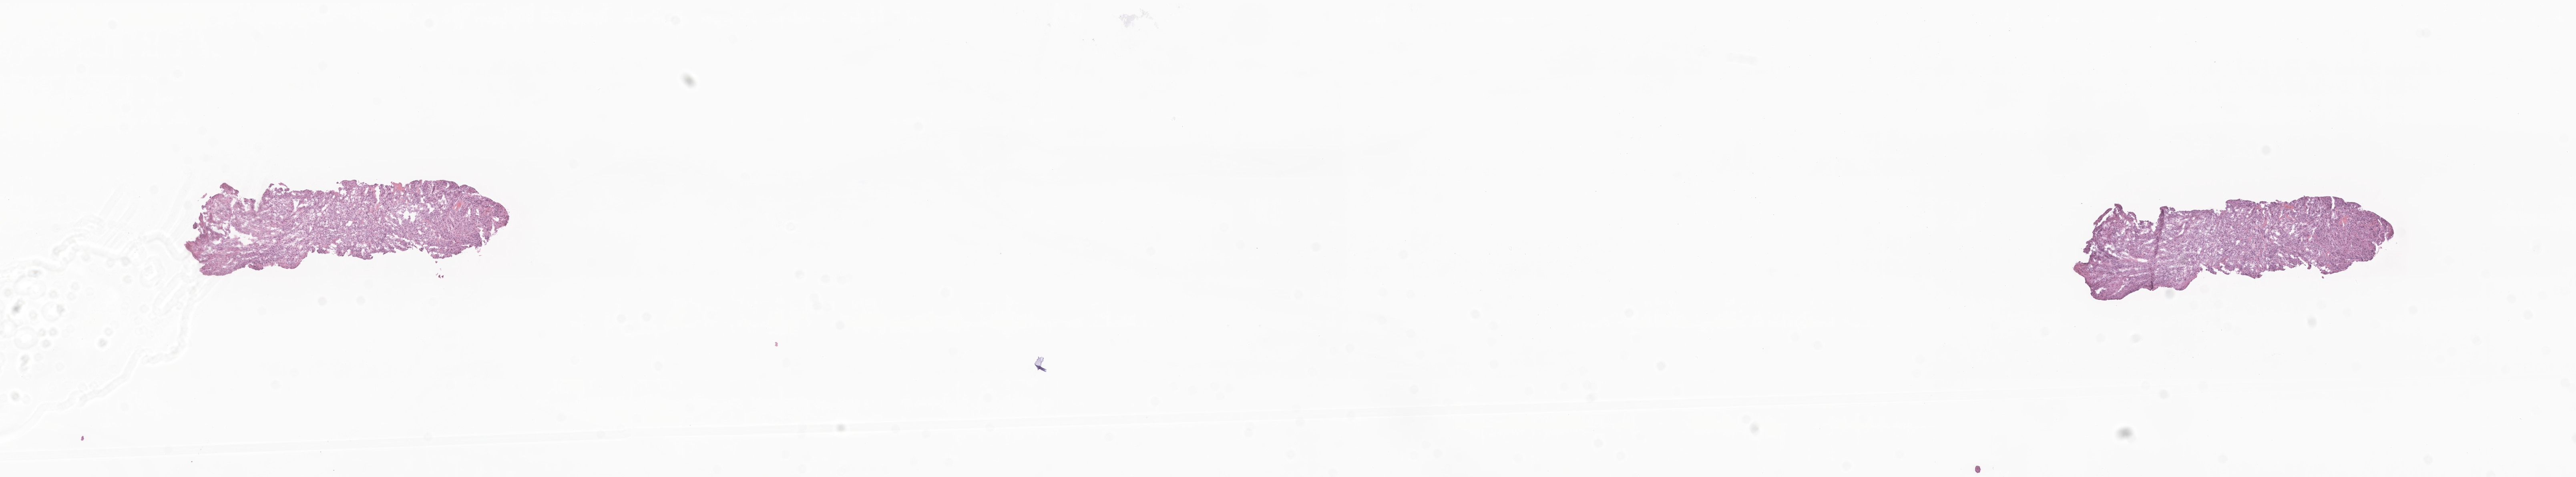
Whole-slide image, haematoxylin and eosin stain of tumor tissue from the soft tissue of lower extremity, whole scanned area (about 27.1 x 5.0 mm) shown as a low-resolution overview, frozen section. Female patient, age 152 months.
Diagnosis: Spindle cell carcinoma, NOS.